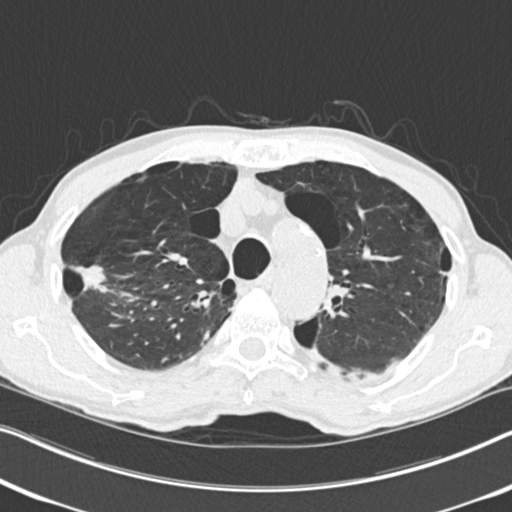
Low-dose screening chest CT, one axial slice. Position 187 of 251 along the scan axis. Lung window (W 1500 / L -600 HU). 2 mm slice thickness. 512 × 512 image matrix, field of view 334 × 334 mm.
Structures marked on this image (expert manual segmentation):
- lesion 1 (tumor, upper lobe of right lung): box from (x=73, y=266) to (x=108, y=293) px